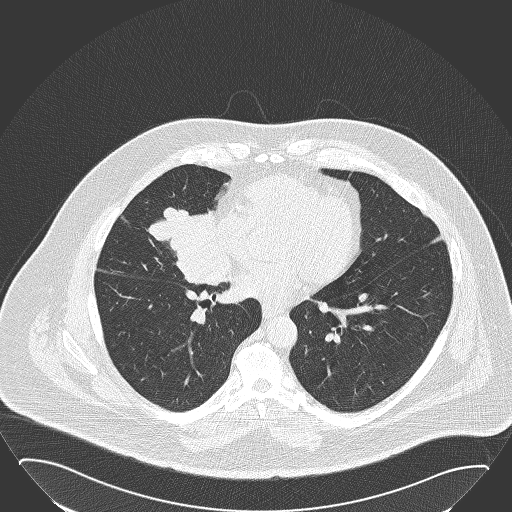
Chest CT (low-dose screening protocol), one axial image, baseline screening round, lung window (W 1500 / L -600 HU), slice 95 of 168 in the series. Male participant, aged 61 years at enrolment. Former smoker at enrolment.
Expert-annotated lung lesion, box from (x=142, y=192) to (x=230, y=279) px. The screening reader recorded 2 non-calcified nodules or masses ≥4 mm on this exam (right middle lobe, left lower lobe); which of them this box marks is not recorded. Official screen result: positive, change unspecified: nodule(s) >= 4 mm or enlarging nodule(s), mass(es), or other non-specific abnormalities suspicious for lung cancer. Lung cancer was diagnosed 47 days after this screen: basaloid squamous cell carcinoma, right middle lobe, right hilum, poorly differentiated (G3), stage IIB (AJCC 6th edition), 95 mm at pathology.